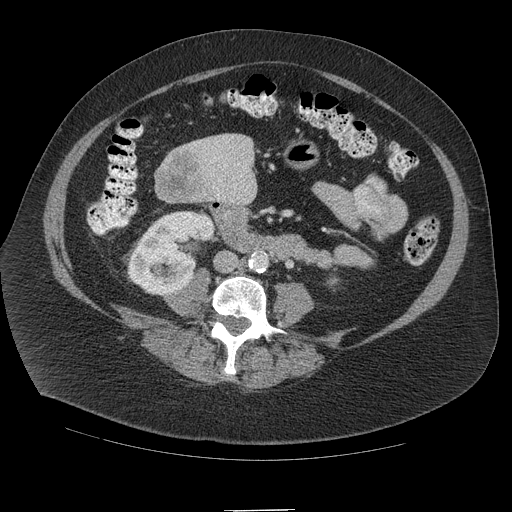
Contrast-enhanced abdominal CT (liver protocol), one axial slice; position 23 of 109 along the scan axis; soft-tissue window (W 400 / L 40 HU); 512 × 512 image matrix, field of view 420 × 420 mm. Case-level facts recorded for this patient, not image findings: diagnosis: hepatocellular carcinoma (patient treated with transarterial chemoembolisation; whether this scan precedes or follows treatment is not stated here); TNM stage (as recorded): Stage-IVB; Child-Pugh class: A.
Outlined on this slice (semi-automatically segmented with operator editing):
- liver parenchyma outside the tumour (the mass and vessels are separate outlines, so this box may not span the whole liver): bounding box <211,134,252,152> (left, top, right, bottom; pixels)